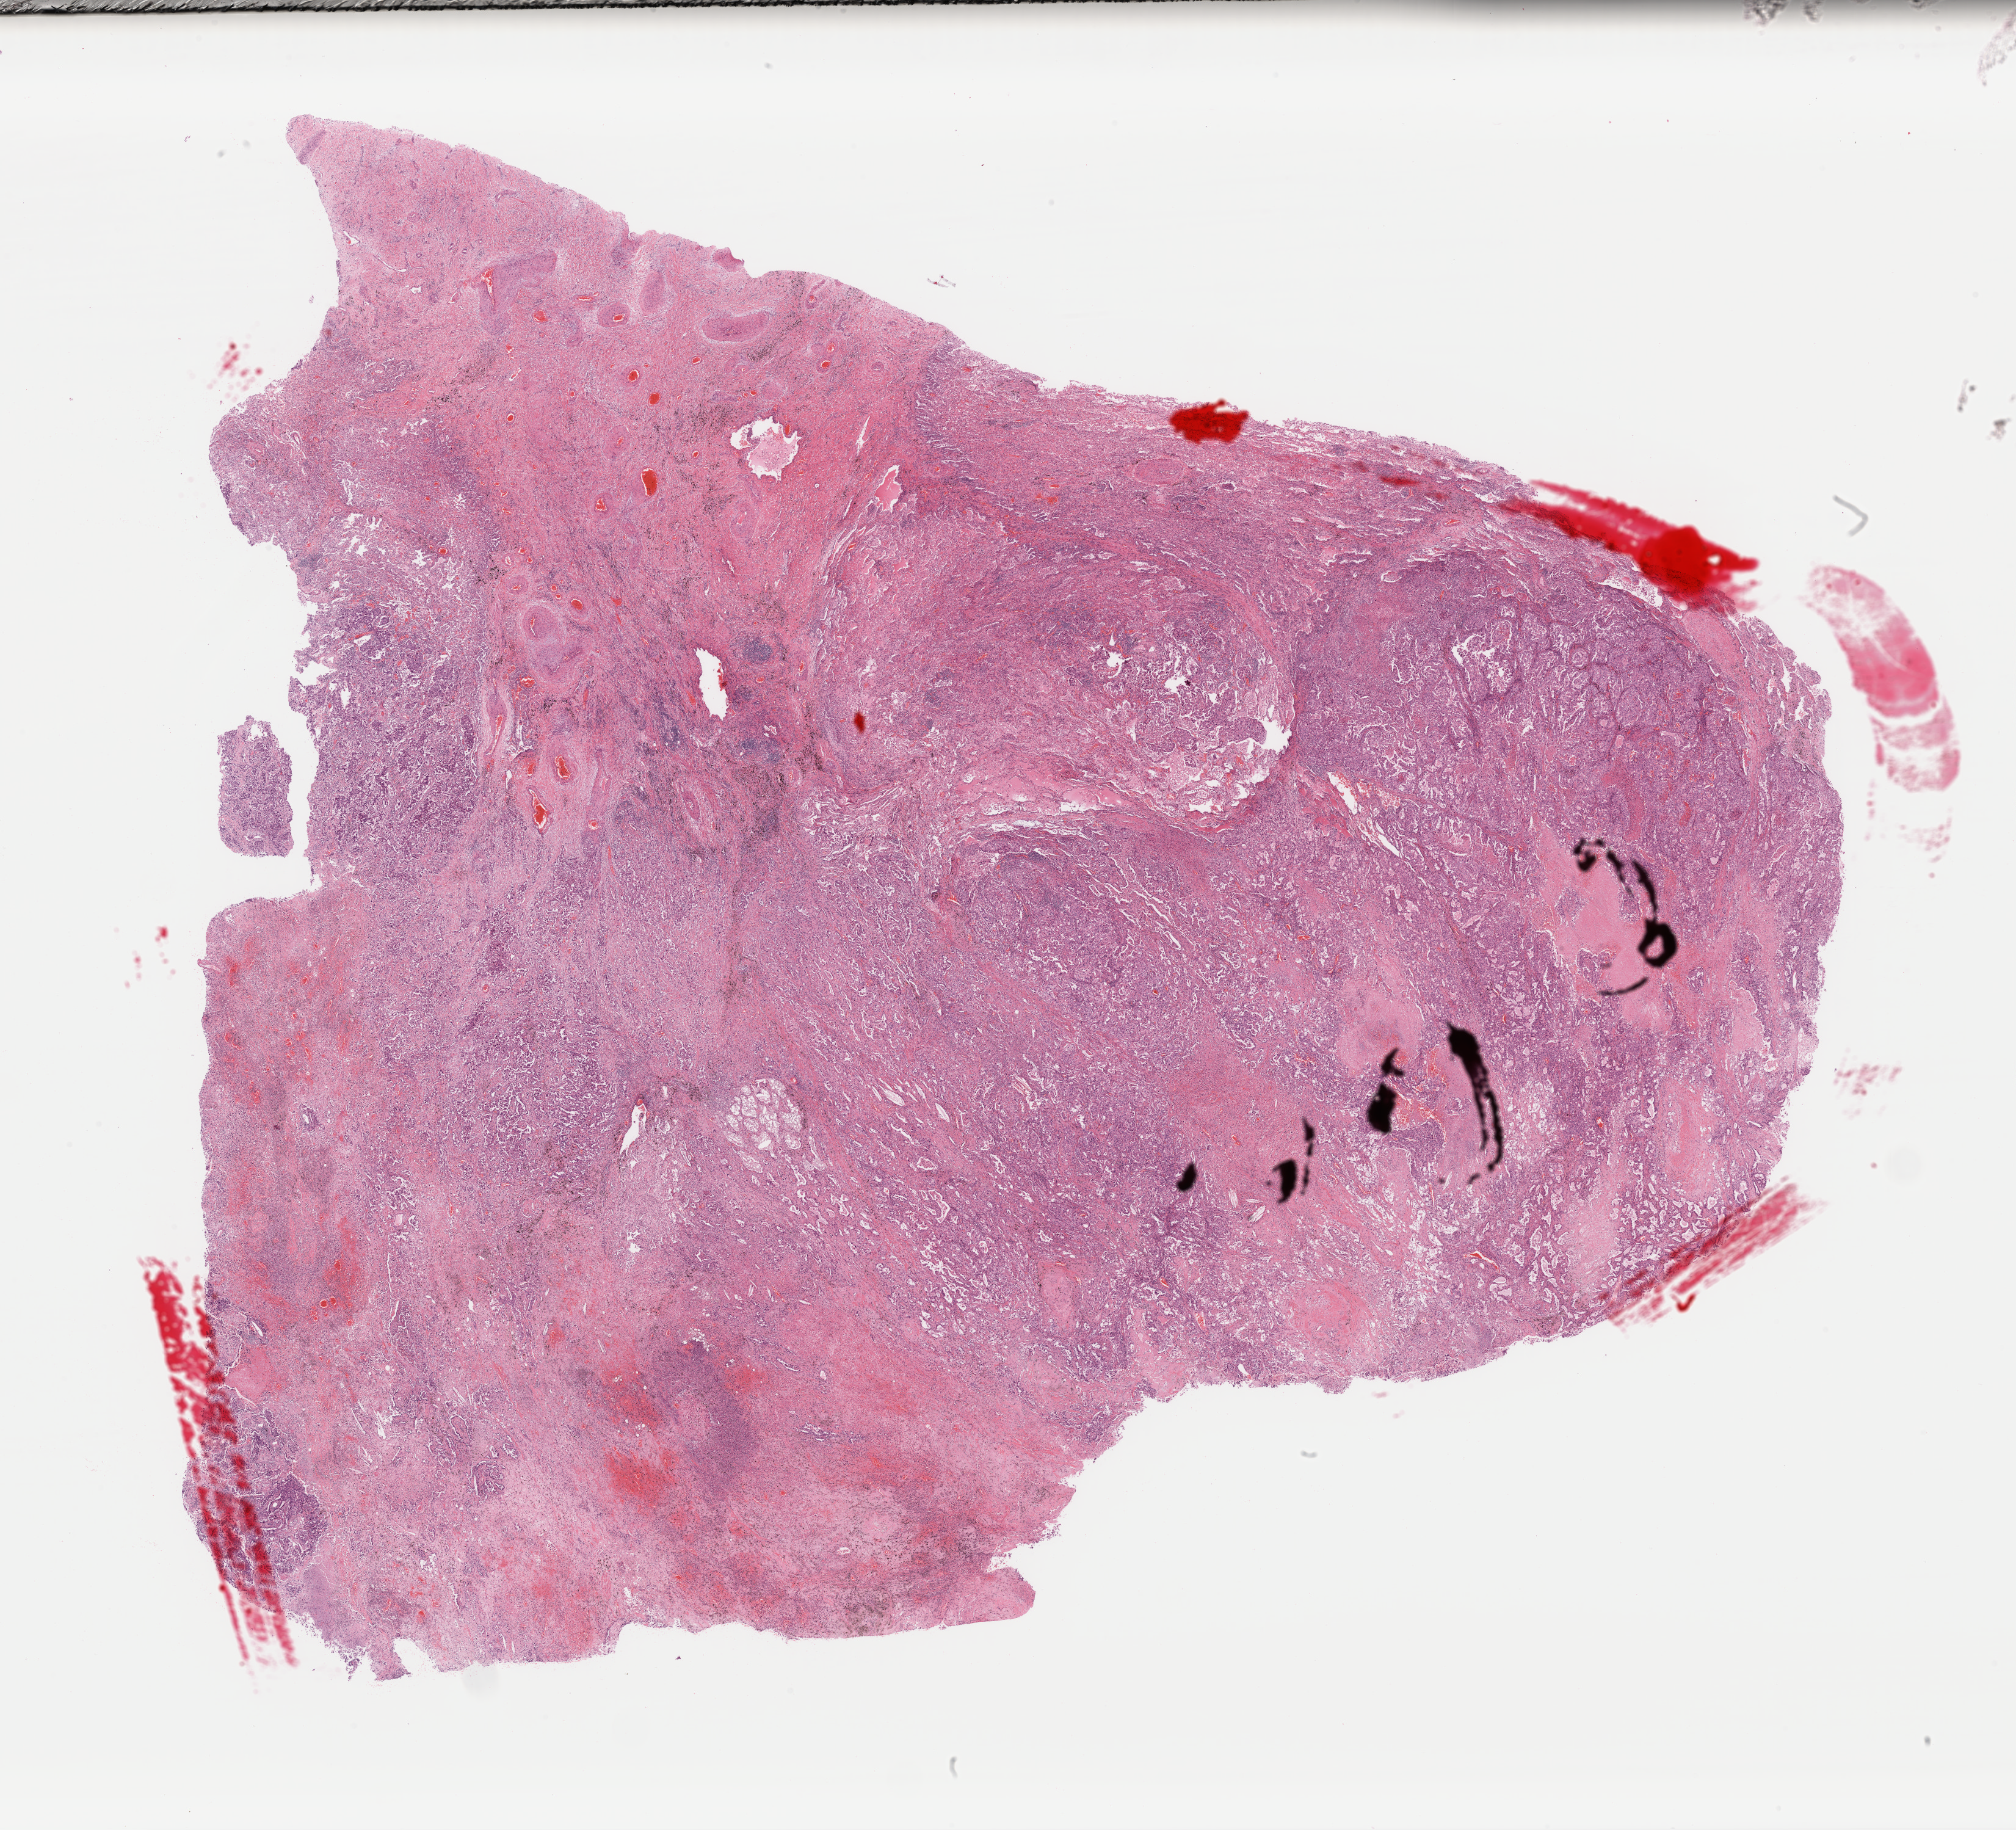
Hematoxylin and eosin (H&E) stained whole-slide image — low-resolution overview of the scanned area, about 26.1 x 23.7 mm (slide scanned at 40x). Formalin-fixed paraffin-embedded (FFPE) diagnostic section. Primary tumour sample from the lung. Male patient; age at initial diagnosis 56 years.
- pathologic diagnosis: Adenocarcinoma, NOS (upper lobe, lung)
- laterality: right
- AJCC pathologic stage: IIB (7th edition)